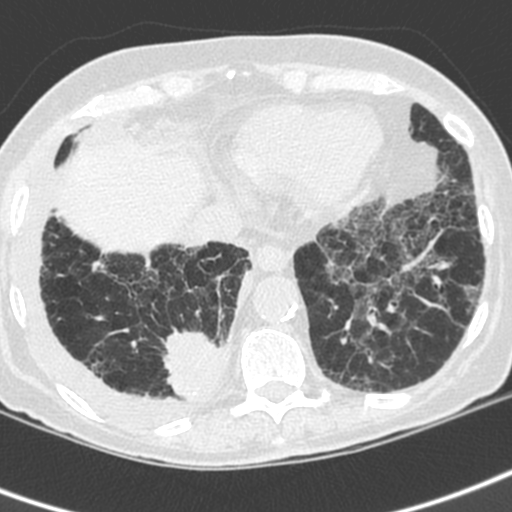
Axial slice from a low-dose chest CT screening exam, first (baseline) screen, lung window (W 1500 / L -600 HU), 1.3 mm slice thickness, standard (soft-tissue) reconstruction kernel (C), 512 × 512 image matrix, field of view 288 × 288 mm. Female, age 73 years at enrolment. Current smoker at enrolment.
• Lesion marked by an expert reader, bounding box <158,322,235,406> (left, top, right, bottom; pixels).
• Screening reader's record for this exam (one nodule recorded; not confirmed to be the boxed lesion): non-calcified nodule or mass ≥4 mm, right lower lobe, 35 × 30 mm, spiculated (stellate) margins, soft tissue attenuation.
• Lung cancer was diagnosed 22 days after this screen: adenocarcinoma, NOS, right lower lobe, stage IV (AJCC 6th edition), 35 mm at pathology.